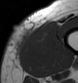
MRI of an extremity soft-tissue mass, one axial slice. Position 9 of 43 along the scan axis. MR volume resampled by the dataset authors to the PET/CT grid (not the native acquisition matrix). 3.27 mm slice thickness. 78 × 83 image matrix, field of view 76 × 81 mm. Male patient. From the clinical record (not read from this slice): histological type: pleiomorphic leiomyosarcoma; grade: high; site of the primary tumour: left thigh.
Structures marked on this image (expert contour drawn on MRI and transferred to this co-registered scan by the dataset authors):
- gross tumour volume including surrounding oedema: bounding box [x1, y1, x2, y2] px = [20, 21, 57, 71]
- gross tumour volume (mass): [24, 26, 53, 57]